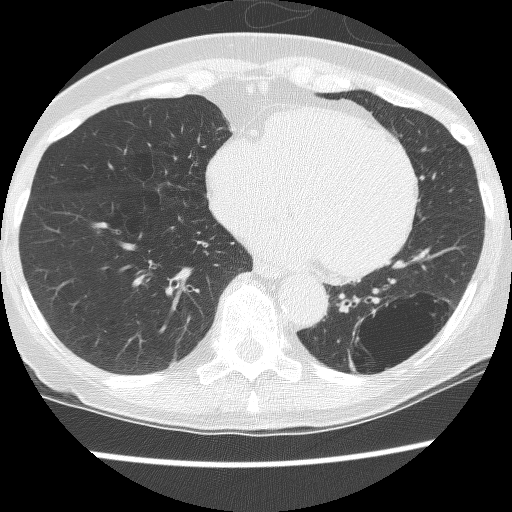
Chest CT (low-dose screening protocol), one axial image, third screening round (two years after baseline), lung window (W 1500 / L -600 HU), 2.5 mm slice thickness, lung (sharp) reconstruction kernel (BONE), slice 87 of 130 in the series, 512 × 512 image matrix. Female, age 61 years at enrolment.
Lesion marked by an expert reader, box from (x=331, y=291) to (x=447, y=389) px. The screening reader recorded 2 non-calcified nodules or masses ≥4 mm on this exam (left lower lobe, left lower lobe); which of them this box marks is not recorded.